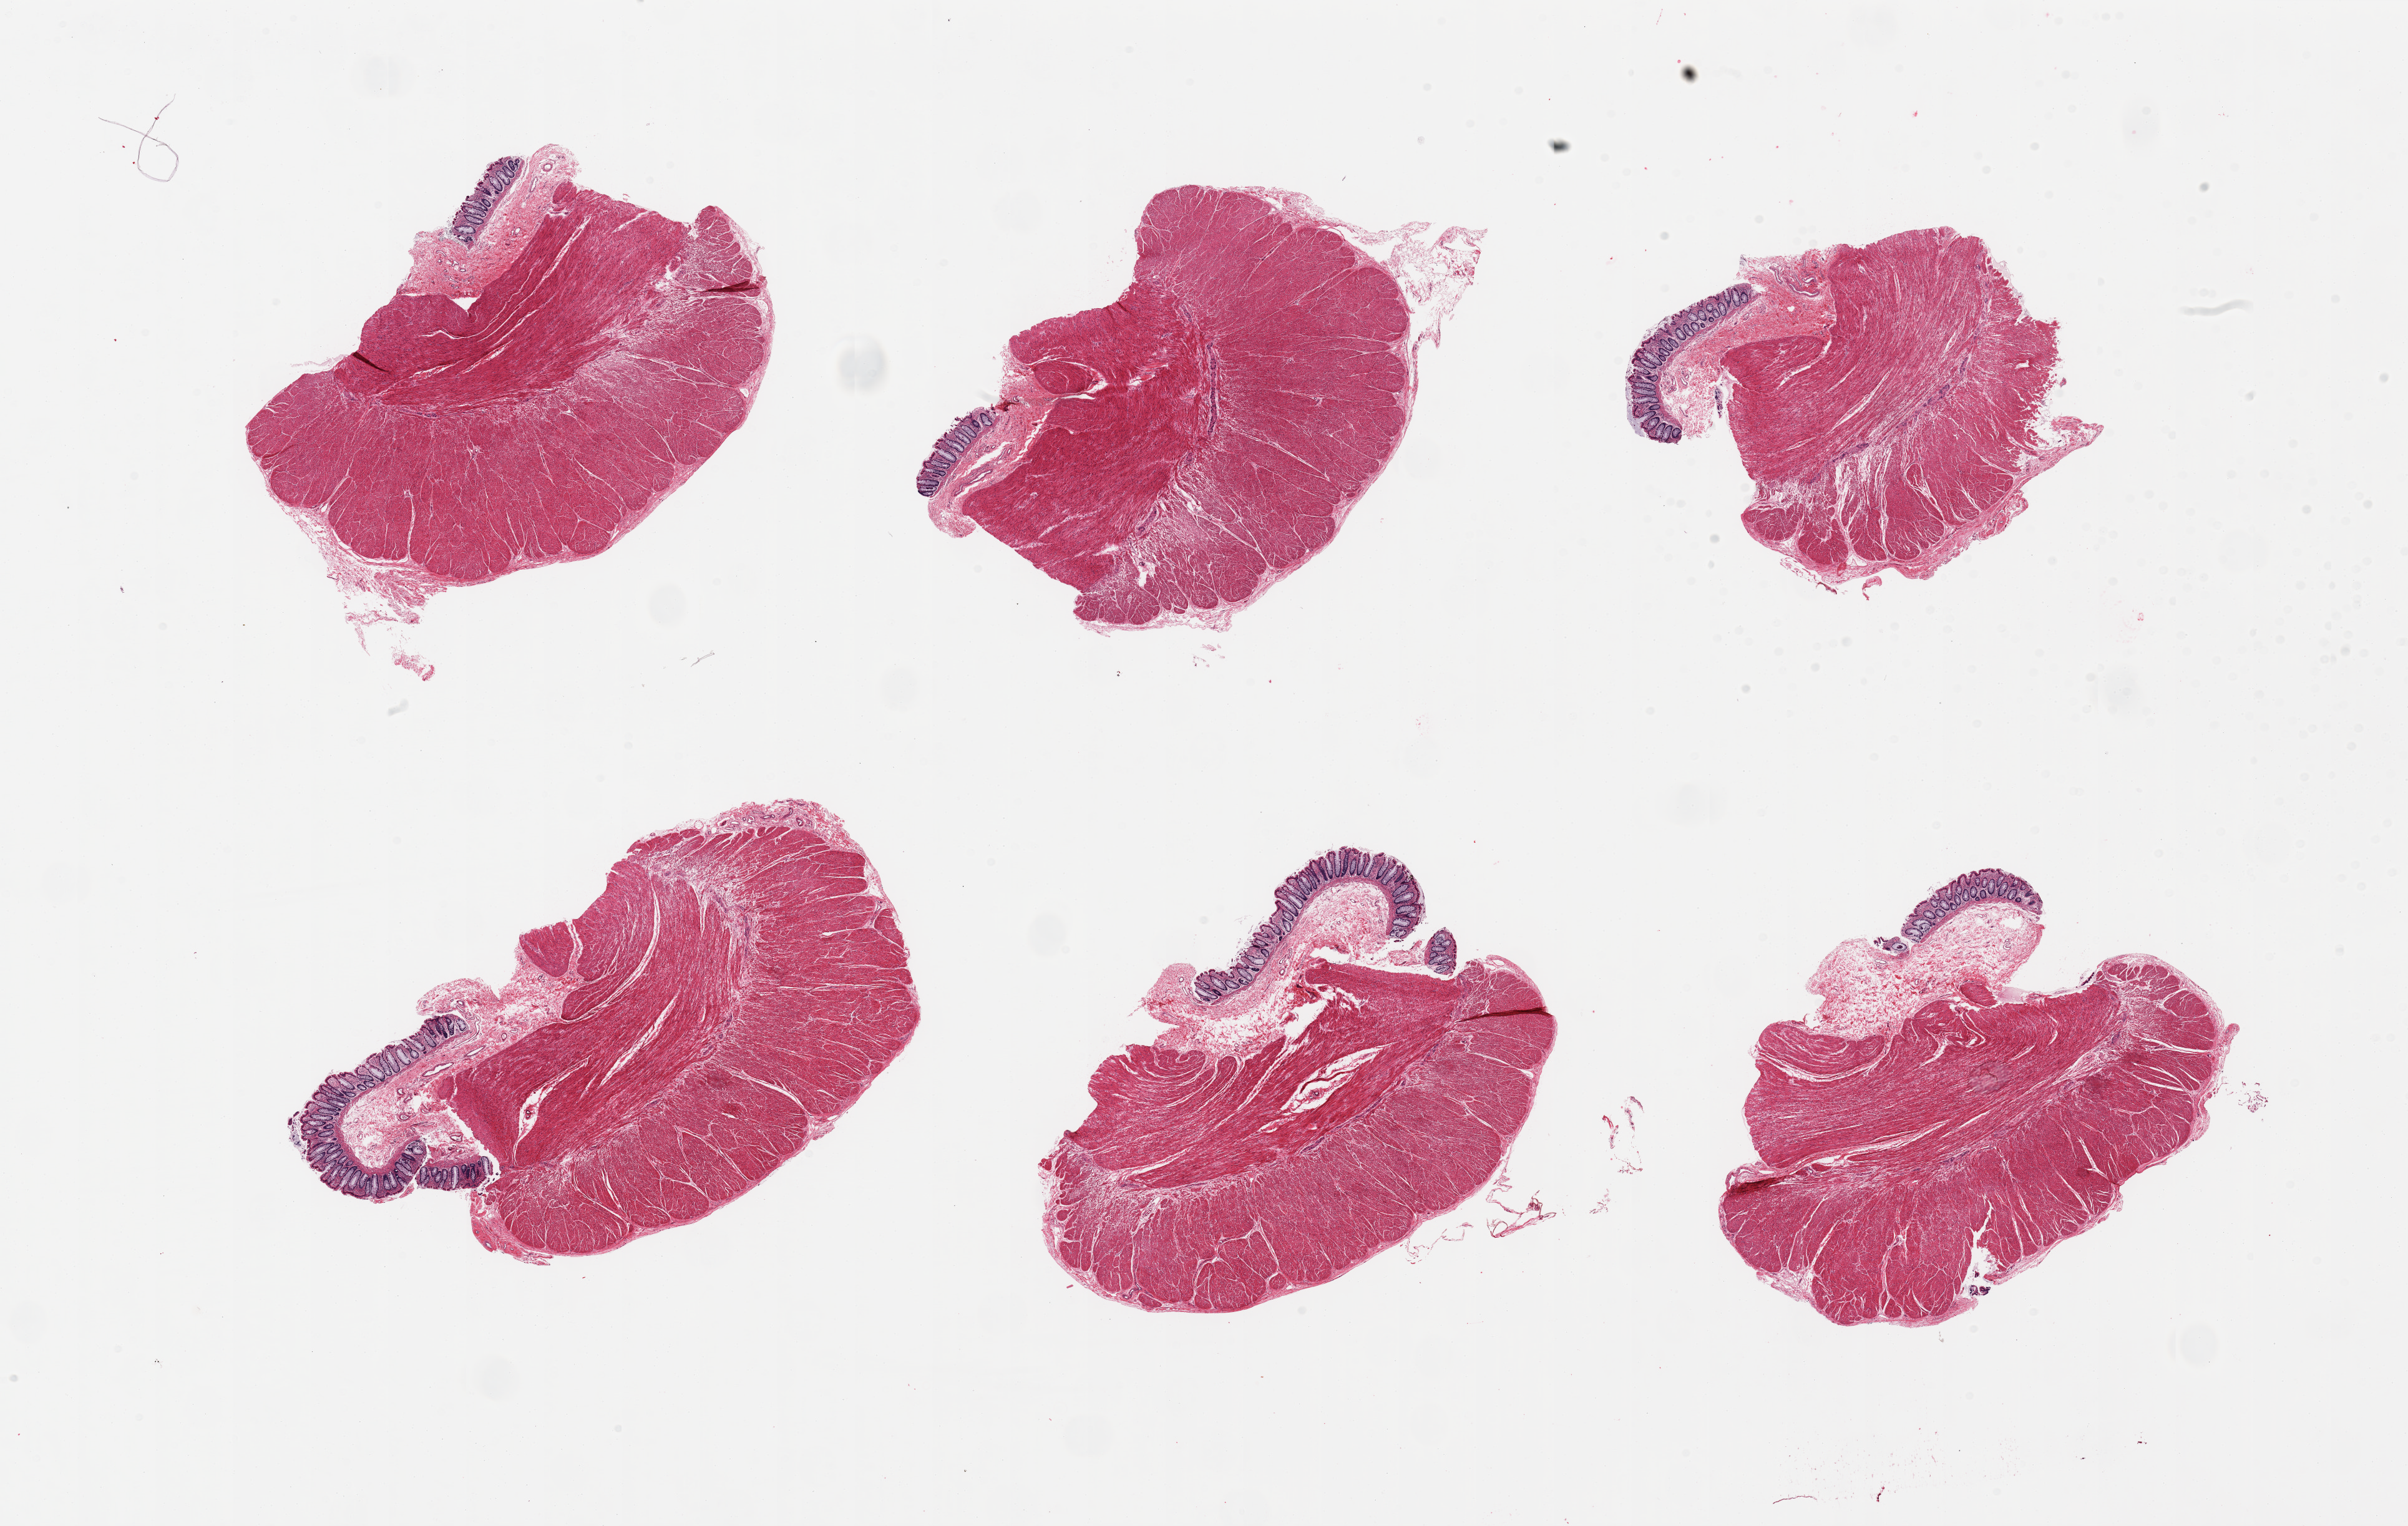
Hematoxylin and eosin (H&E) whole-slide image, shown as a low-resolution overview of the whole scanned area (about 30.5 x 19.3 mm, slide scanned at 20x); PAXgene-fixed, paraffin-embedded tissue; target tissue: transverse colon; tissue donor sample.
- pathologist's review note for this sample: 6 pieces; all full thickness, but mucosa is limited in some